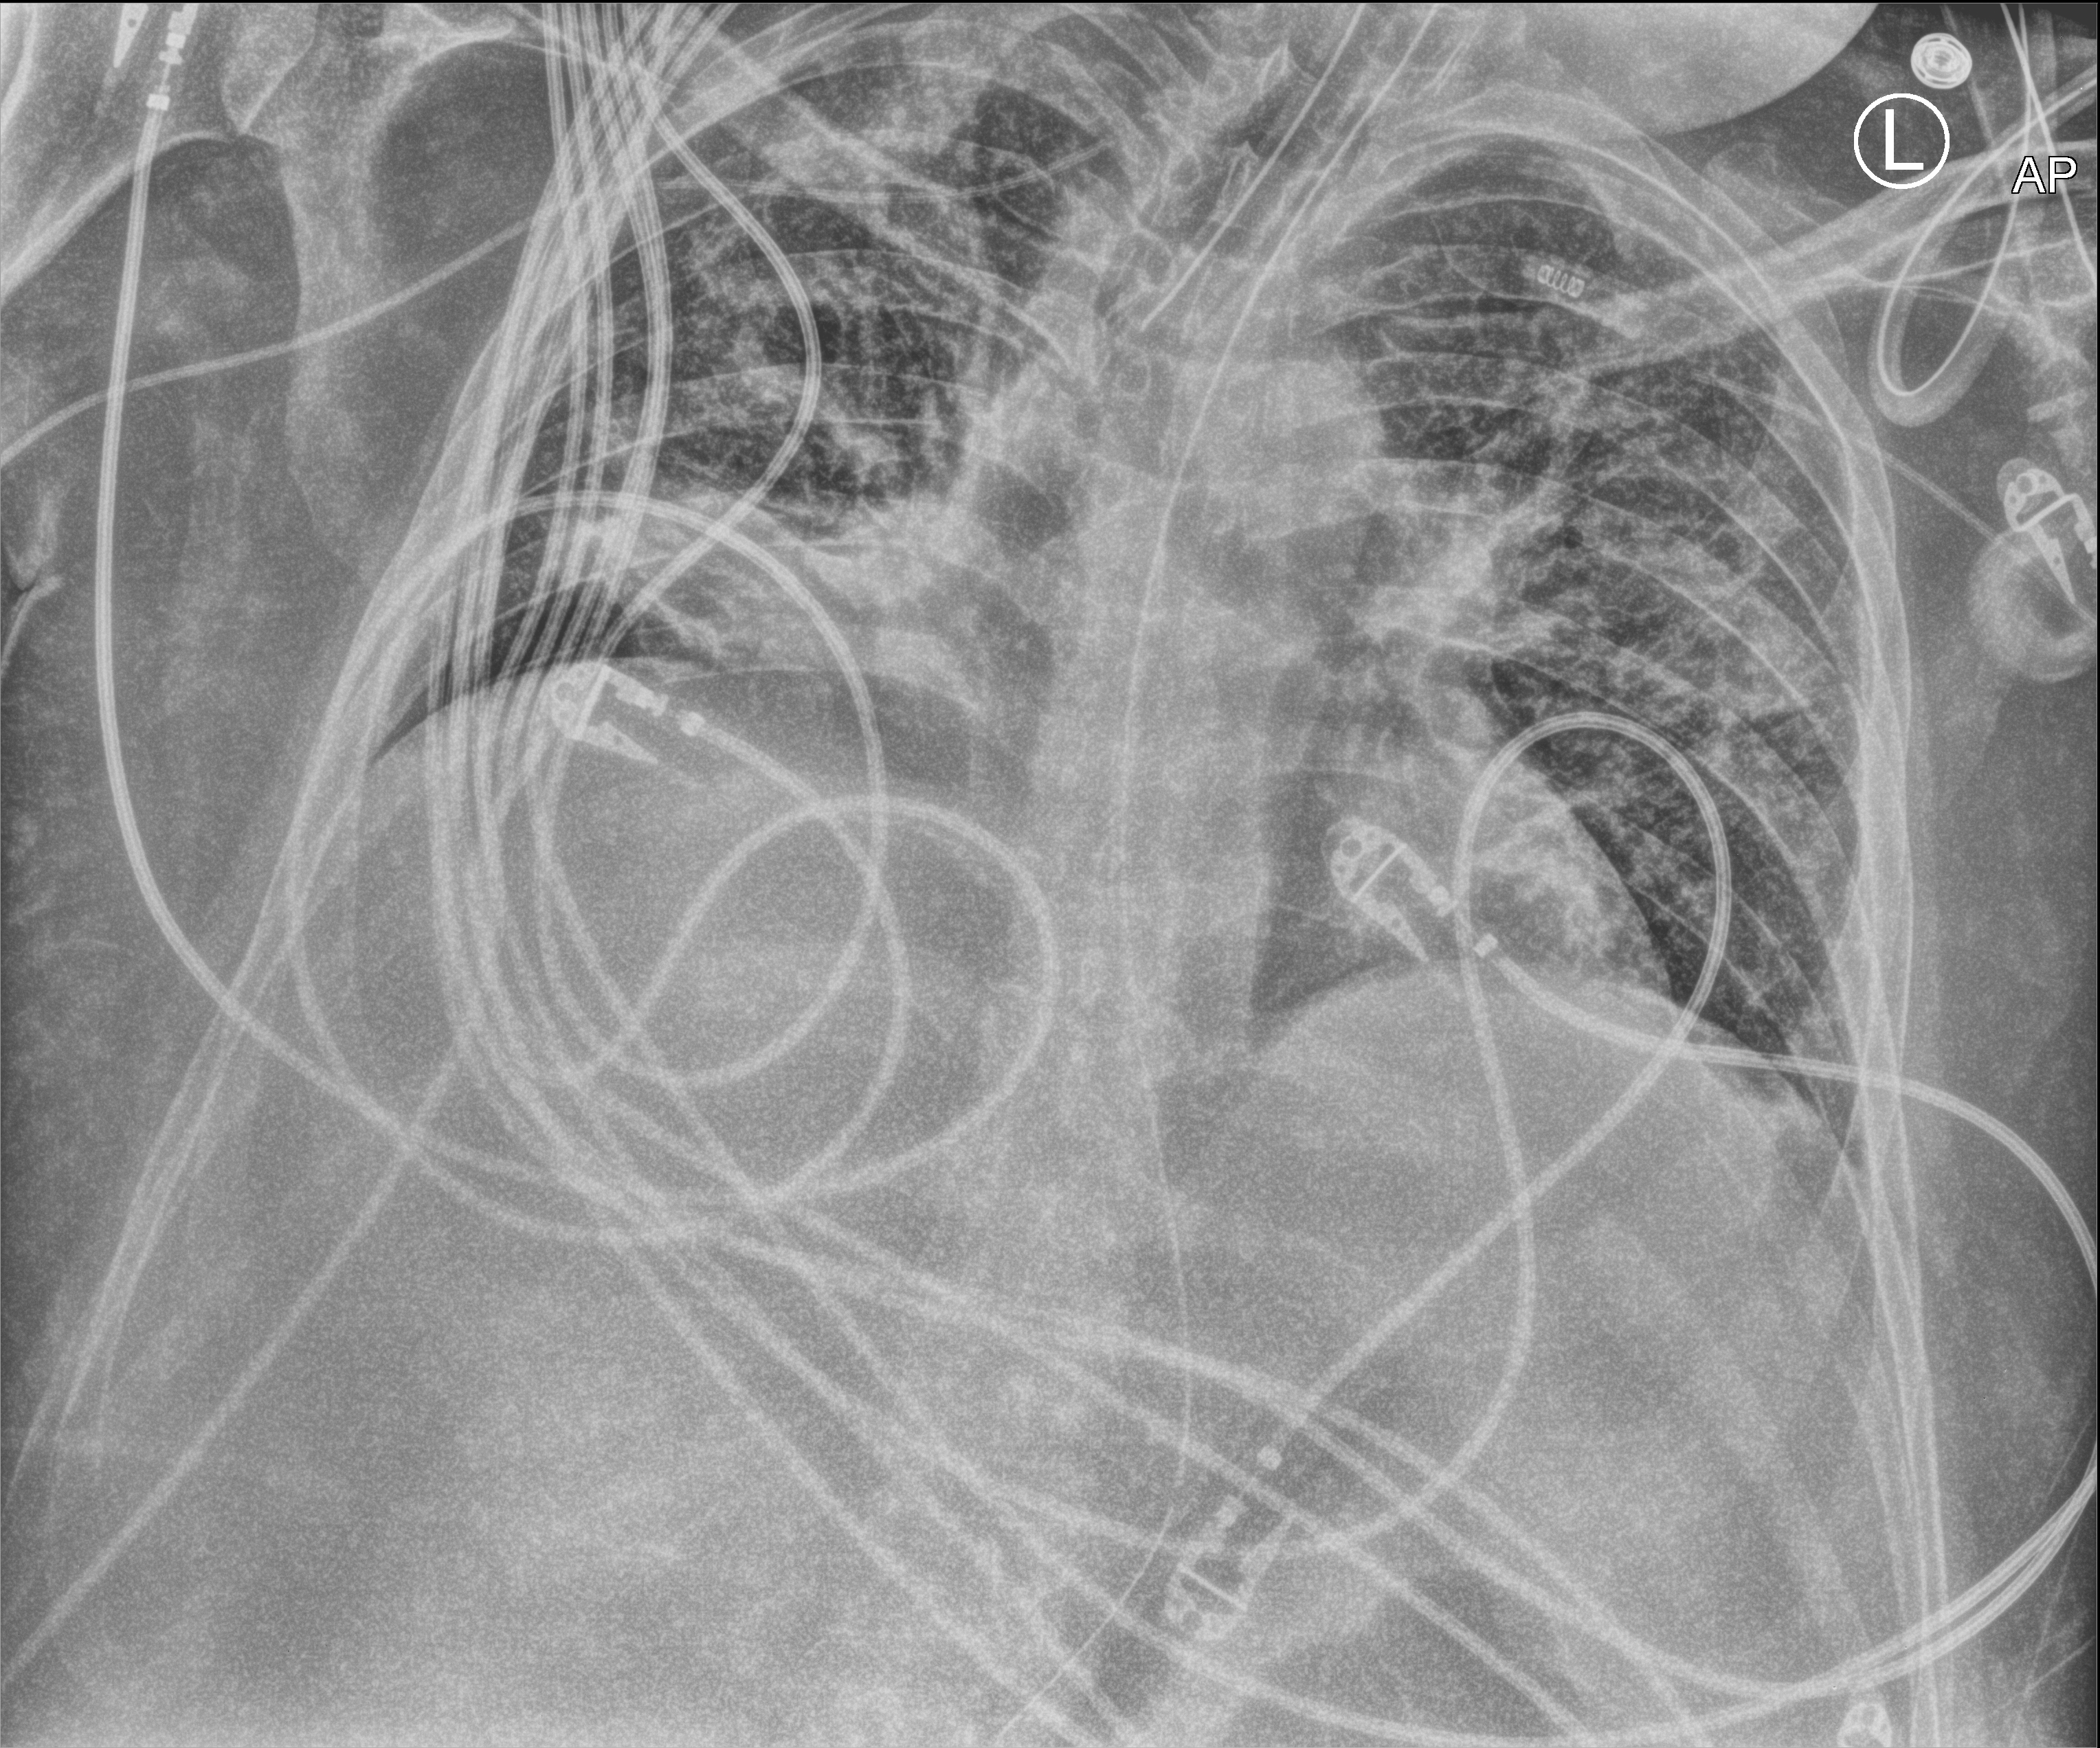
Chest X-ray (portable). Patient hospitalised with COVID-19, aged 18–59 years.
Admission-level facts for this patient (not findings on this image; timing relative to this image not recorded):
- other chronic lung disease (admission record): yes